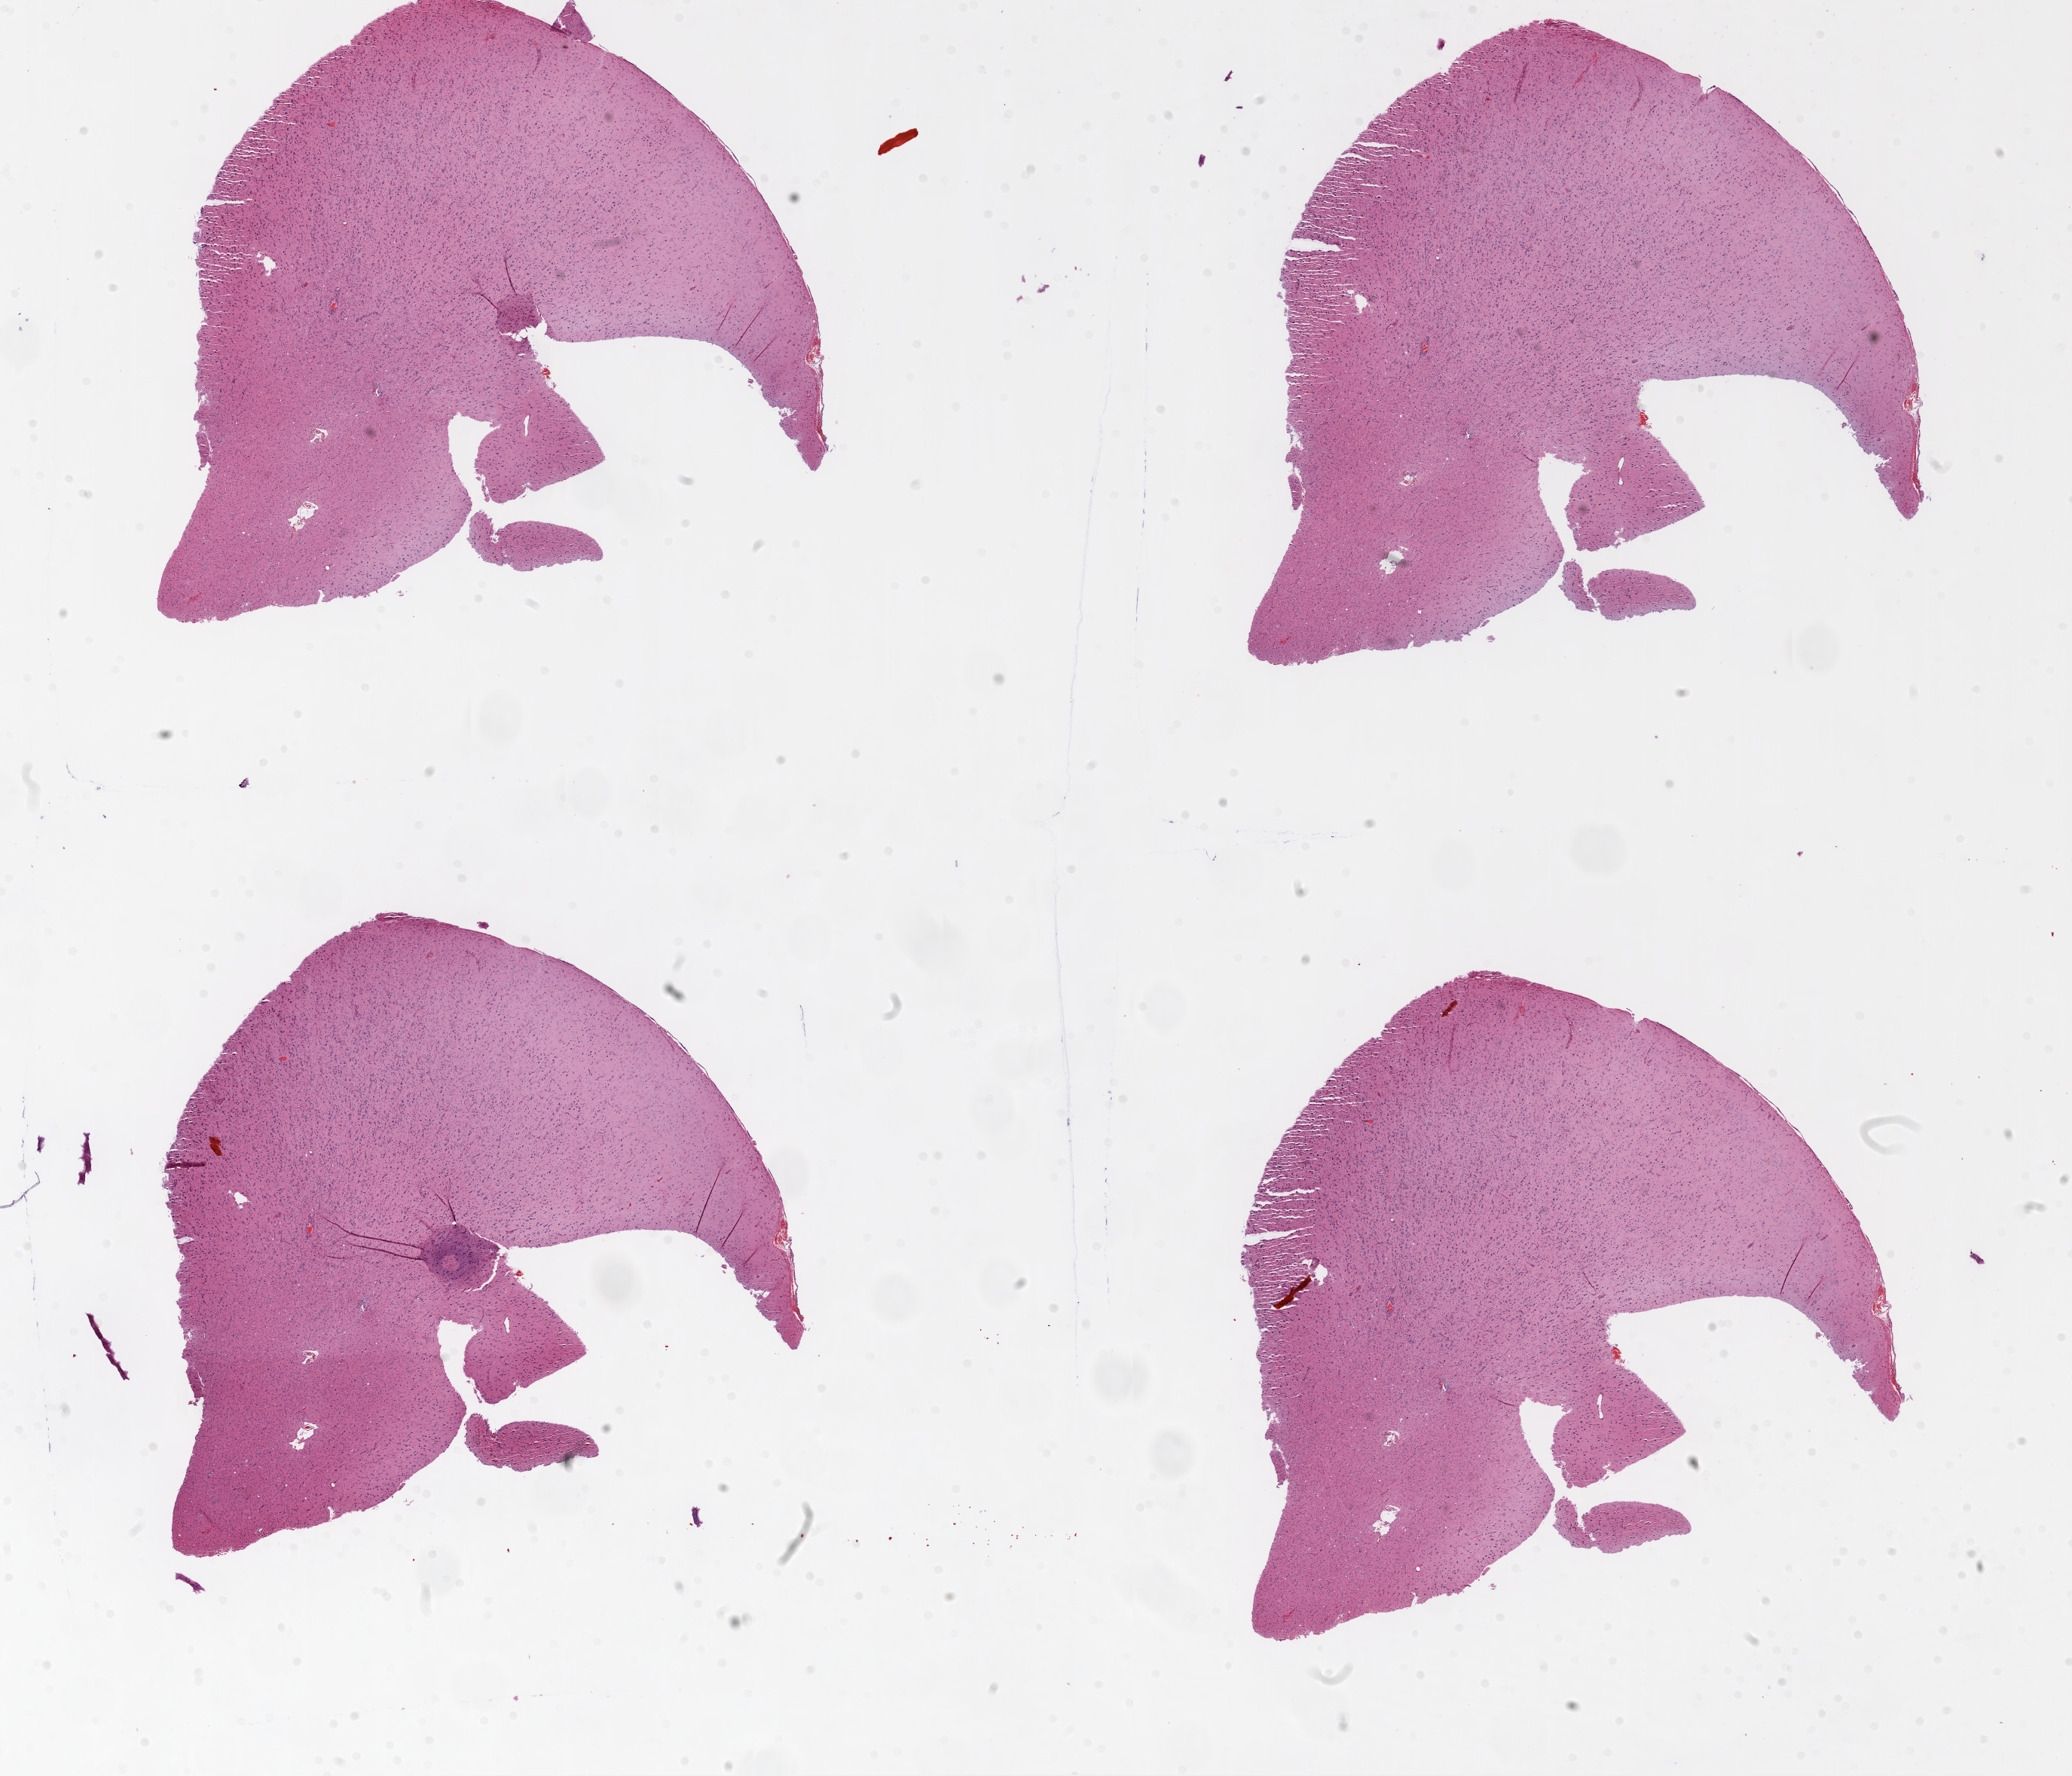
Whole-slide histology image, Hematoxylin and eosin (H&E) stained — shown as a low-resolution overview of the whole scanned area (about 22.1 x 18.9 mm). FFPE section. Sample: primary tumour, brain. Patient: male, age at initial diagnosis 78 years.
Diagnosis: Glioblastoma.